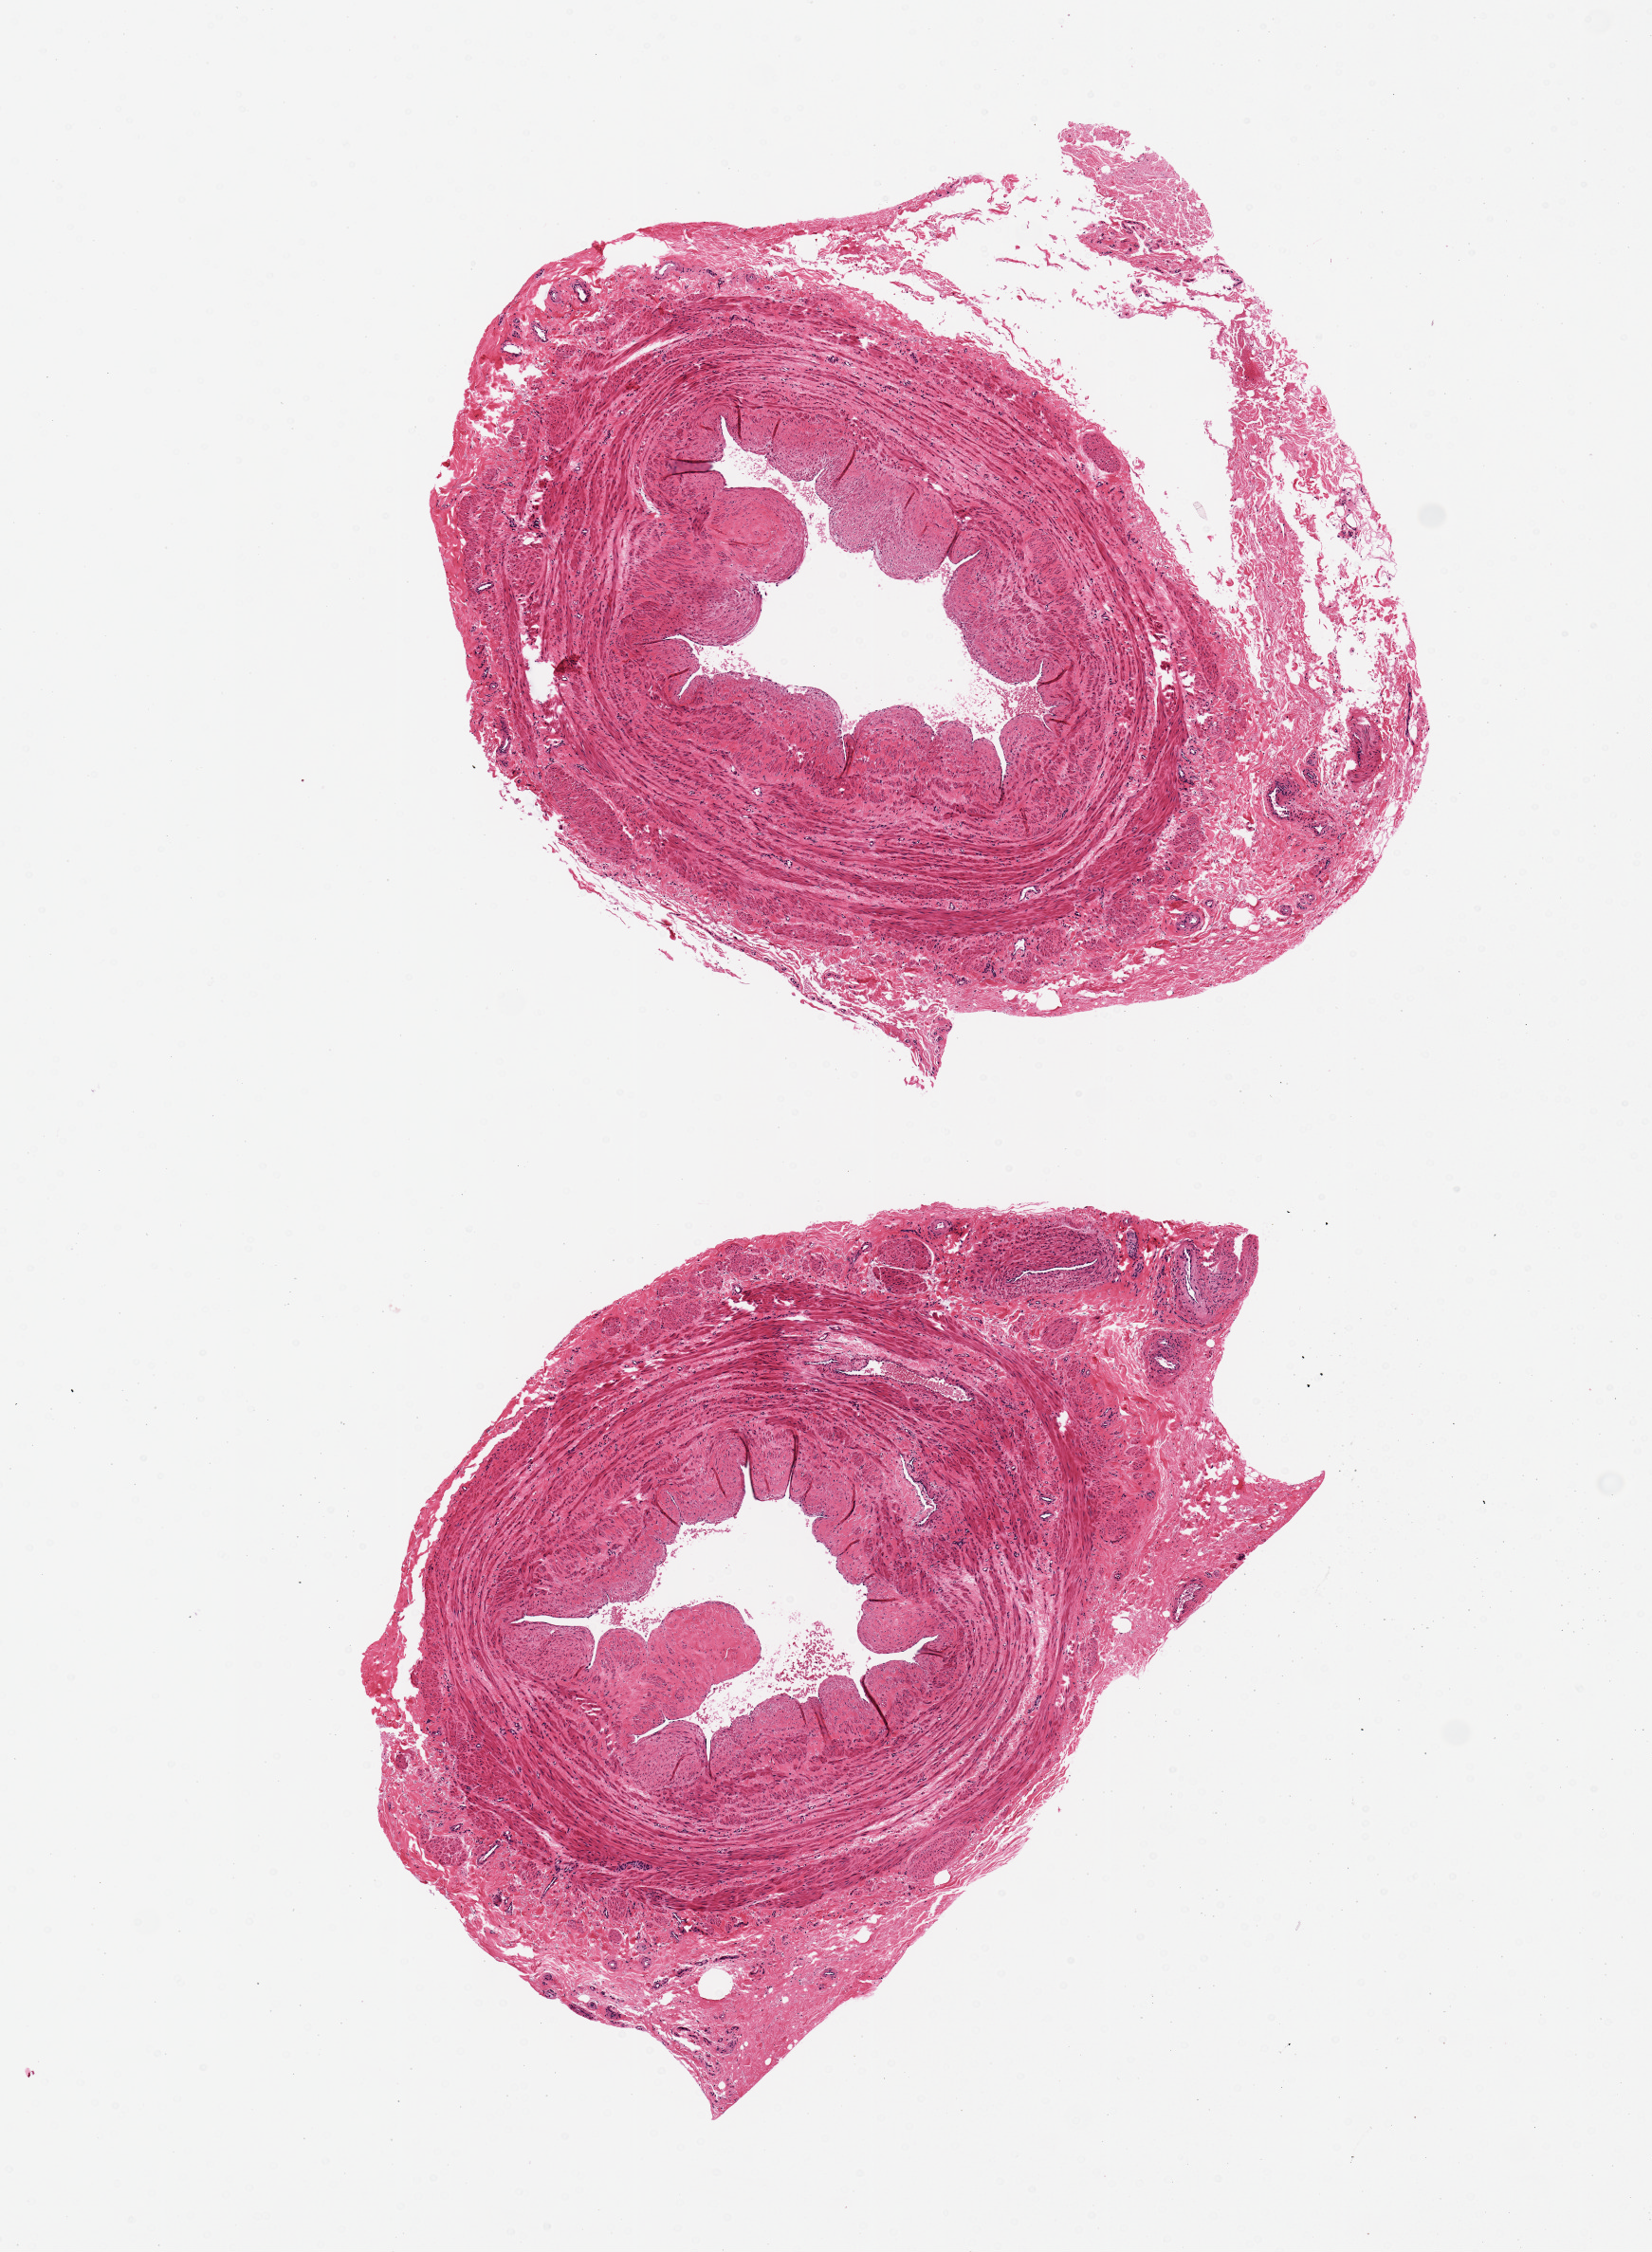
Digitized H&E-stained section — a low-resolution overview of the entire scanned area, about 6.9 x 9.4 mm (from a 20x scan). PAXgene-fixed paraffin-embedded (PFPE) section. Target tissue: tibial artery. Donor tissue sample. Male donor.
Reviewer comment on this tissue sample: Prominent atherosclerotic narrowing (~40%). Vessel is central 75% of specimen; peripheral fat/connective tissue.